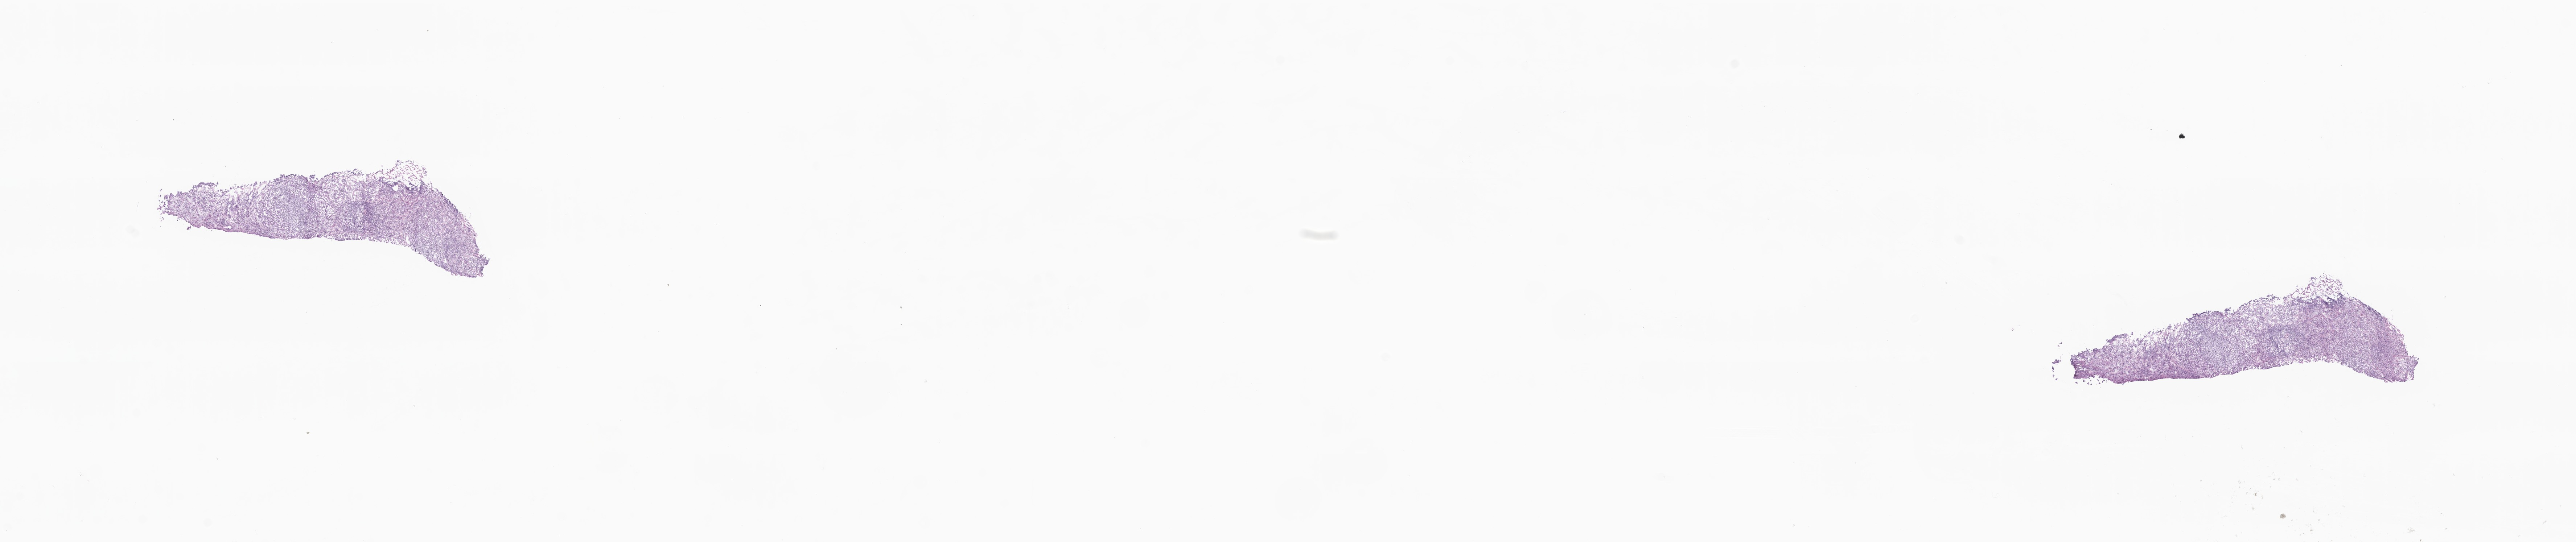
Digitized H&E-stained section, whole scanned area (about 29.9 x 6.3 mm) shown as a low-resolution overview. Cryosection. Specimen: metastatic tumor tissue. Female patient. Composition of this section per pathologist review: tumor cells 76%, tumor nuclei 83%, stromal cells 9%, necrosis 0%, normal cells 15%. Inflammatory infiltration, as recorded: lymphocyte infiltration 27%, monocyte infiltration 4%, neutrophil infiltration 0%.
Patient diagnosis (primary): Lobular carcinoma, NOS. Section: top of the tissue portion.